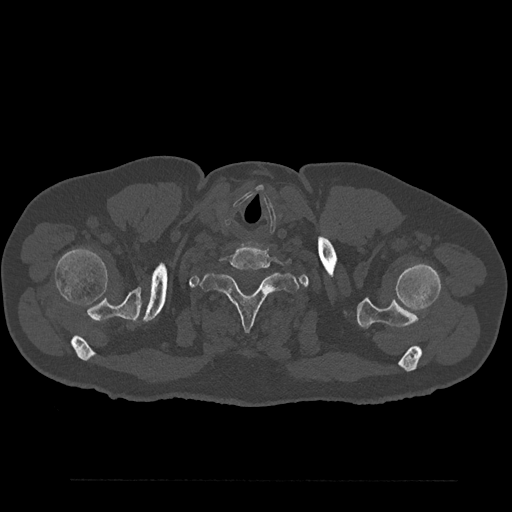
CT including the spine, one axial slice. Position 758 of 797 along the scan axis. Reconstruction kernel Br40s/3. Bone window (W 1800 / L 400 HU). 0.5 mm slice thickness. 512 × 512 image matrix, field of view 430 × 430 mm. Male patient, age 61 years. Case-level facts recorded for this patient, not image findings: primary cancer: prostate.
Annotated regions visible in this slice (semi-automatic segmentation, software-assisted and operator-edited):
- T1 vertebra: box from (x=200, y=261) to (x=299, y=332) px